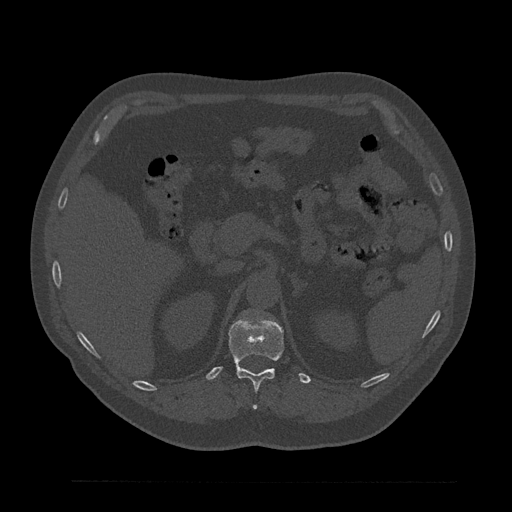
CT including the spine, one axial slice; position 222 of 797 along the scan axis; 120 kVp; bone window (W 1800 / L 400 HU); 0.5 mm slice thickness; 512 × 512 image matrix, field of view 430 × 430 mm. Male patient, age 61 years. Case-level facts recorded for this patient, not image findings: primary cancer: prostate.
Structures marked on this image (semi-automatically segmented with operator editing):
- T12 vertebra: box from (x=229, y=317) to (x=284, y=409) px